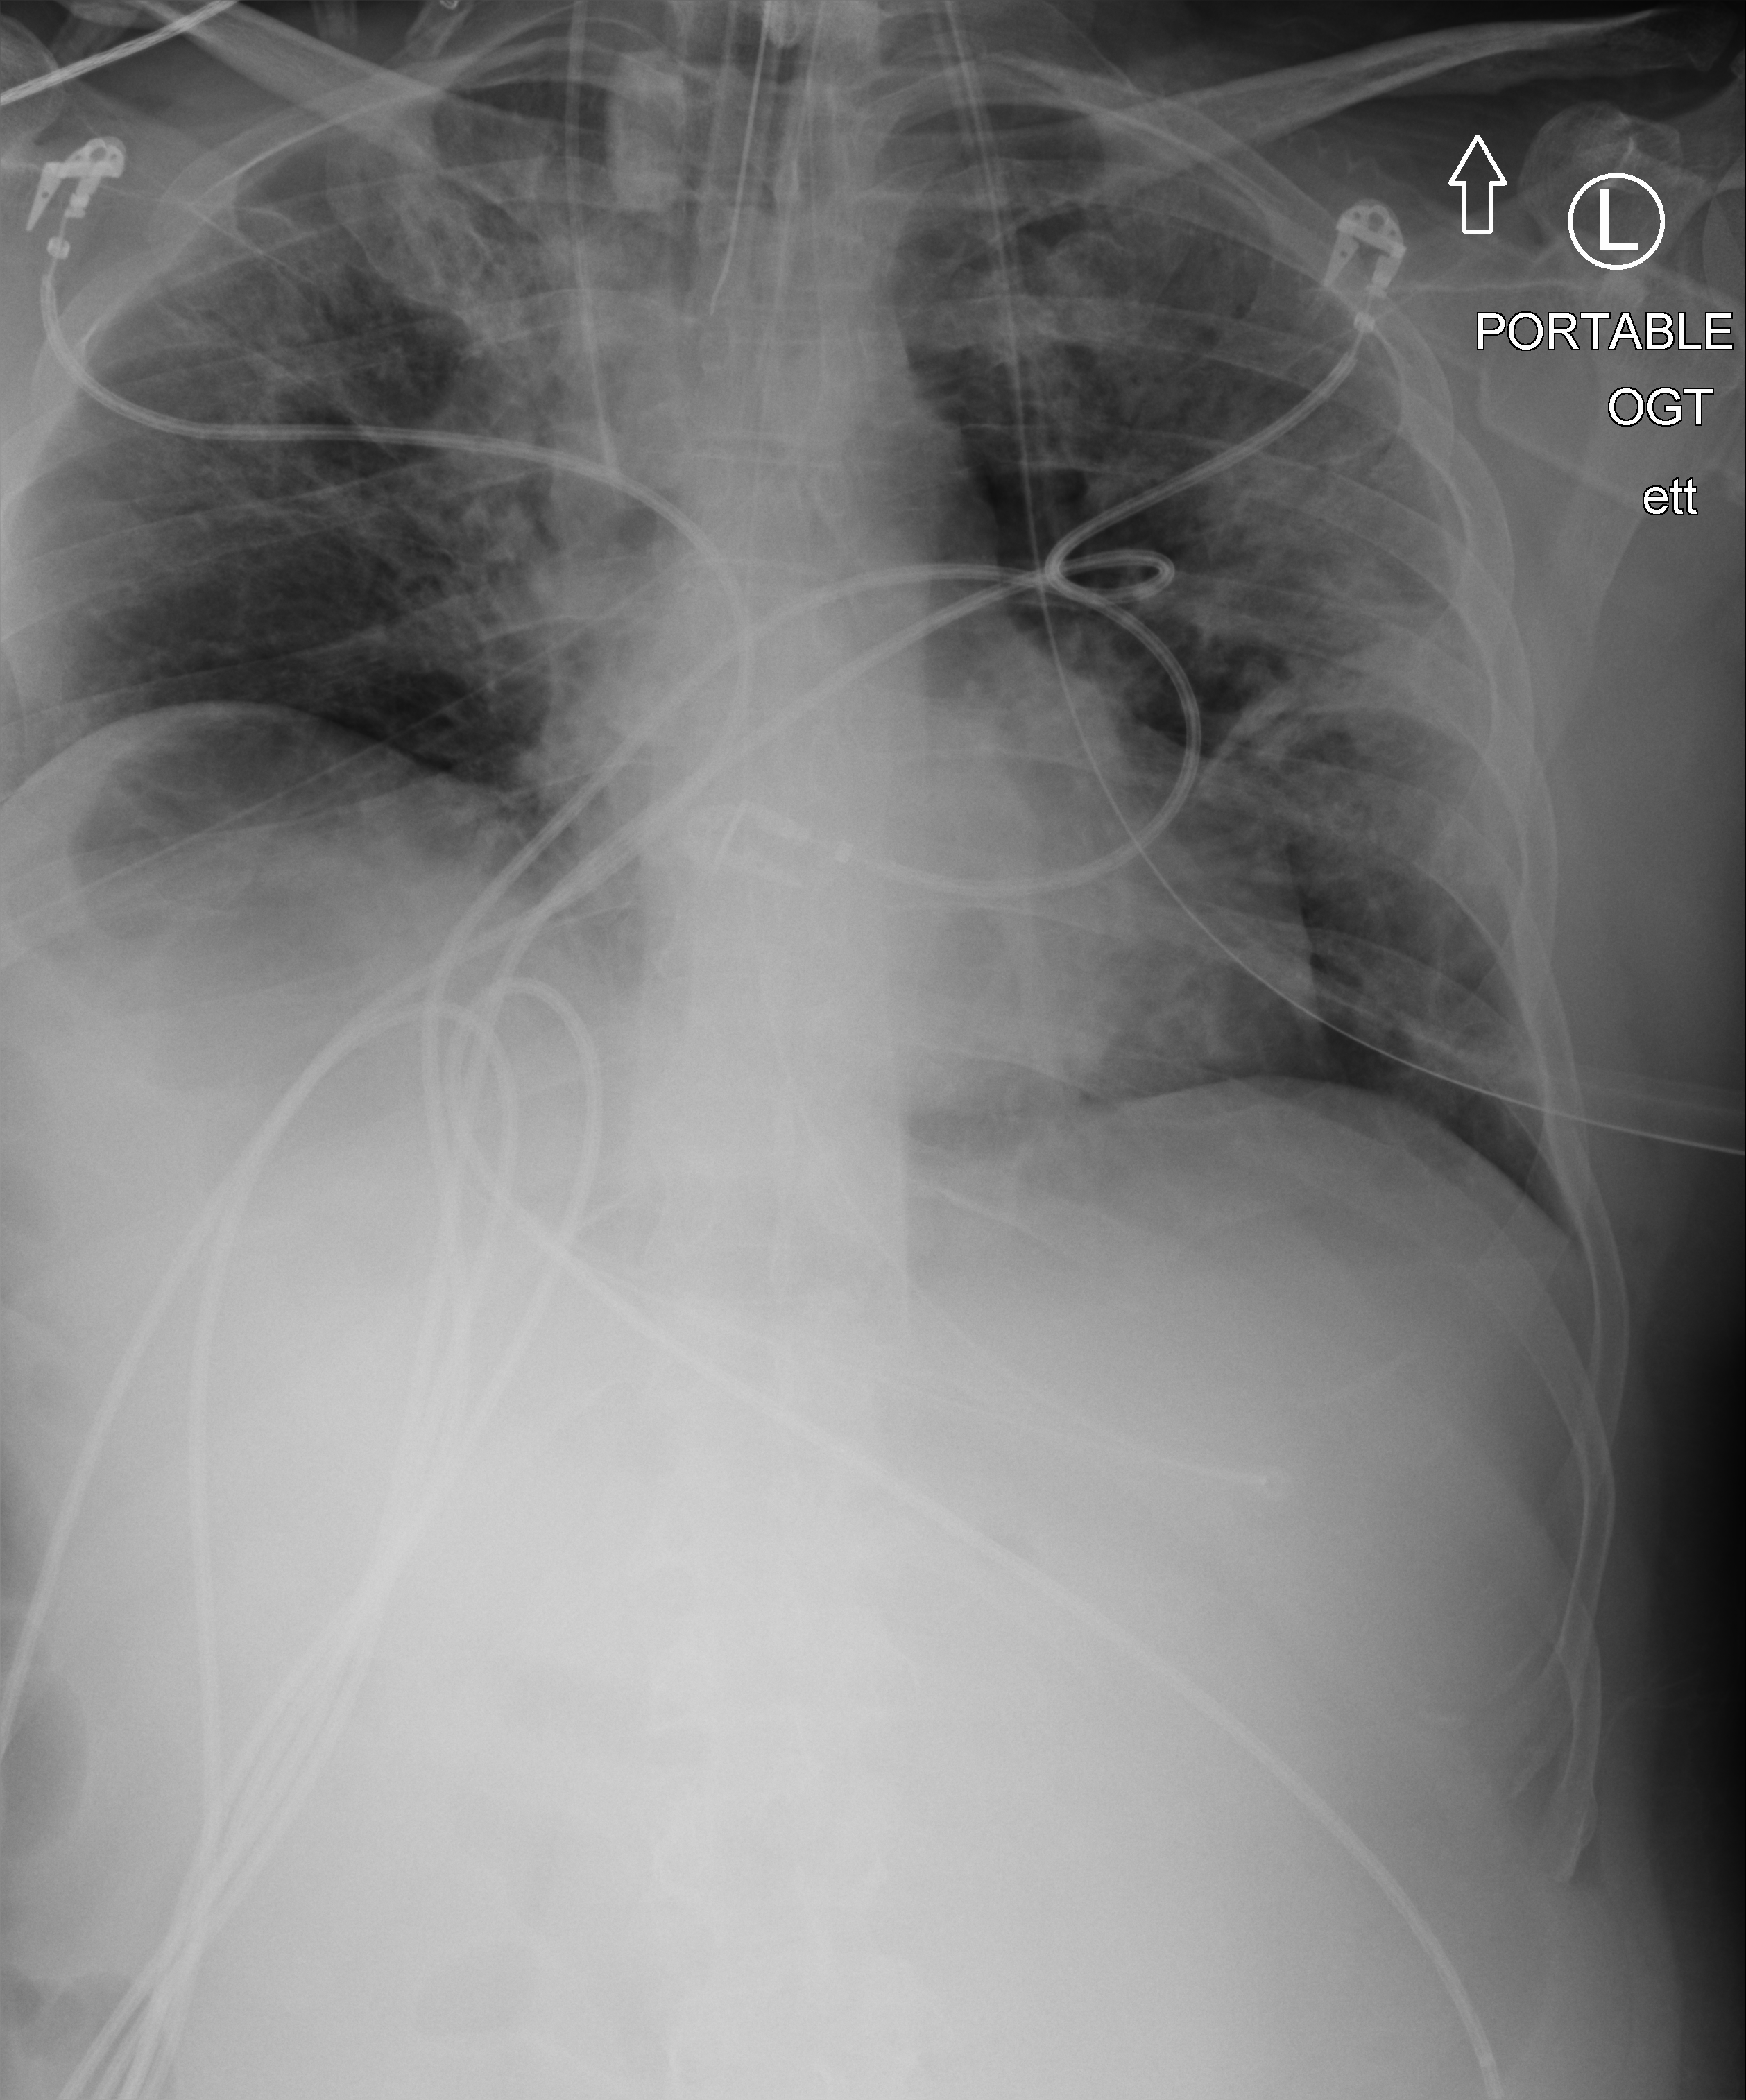
Chest X-ray (portable). Patient hospitalised with COVID-19; male, aged 18–59 years.
Admission-level facts for this patient (not findings on this image; timing relative to this image not recorded): admitted to intensive care during this hospital stay: yes; chronic kidney disease (admission record): no; mechanically ventilated during this hospital stay: yes.